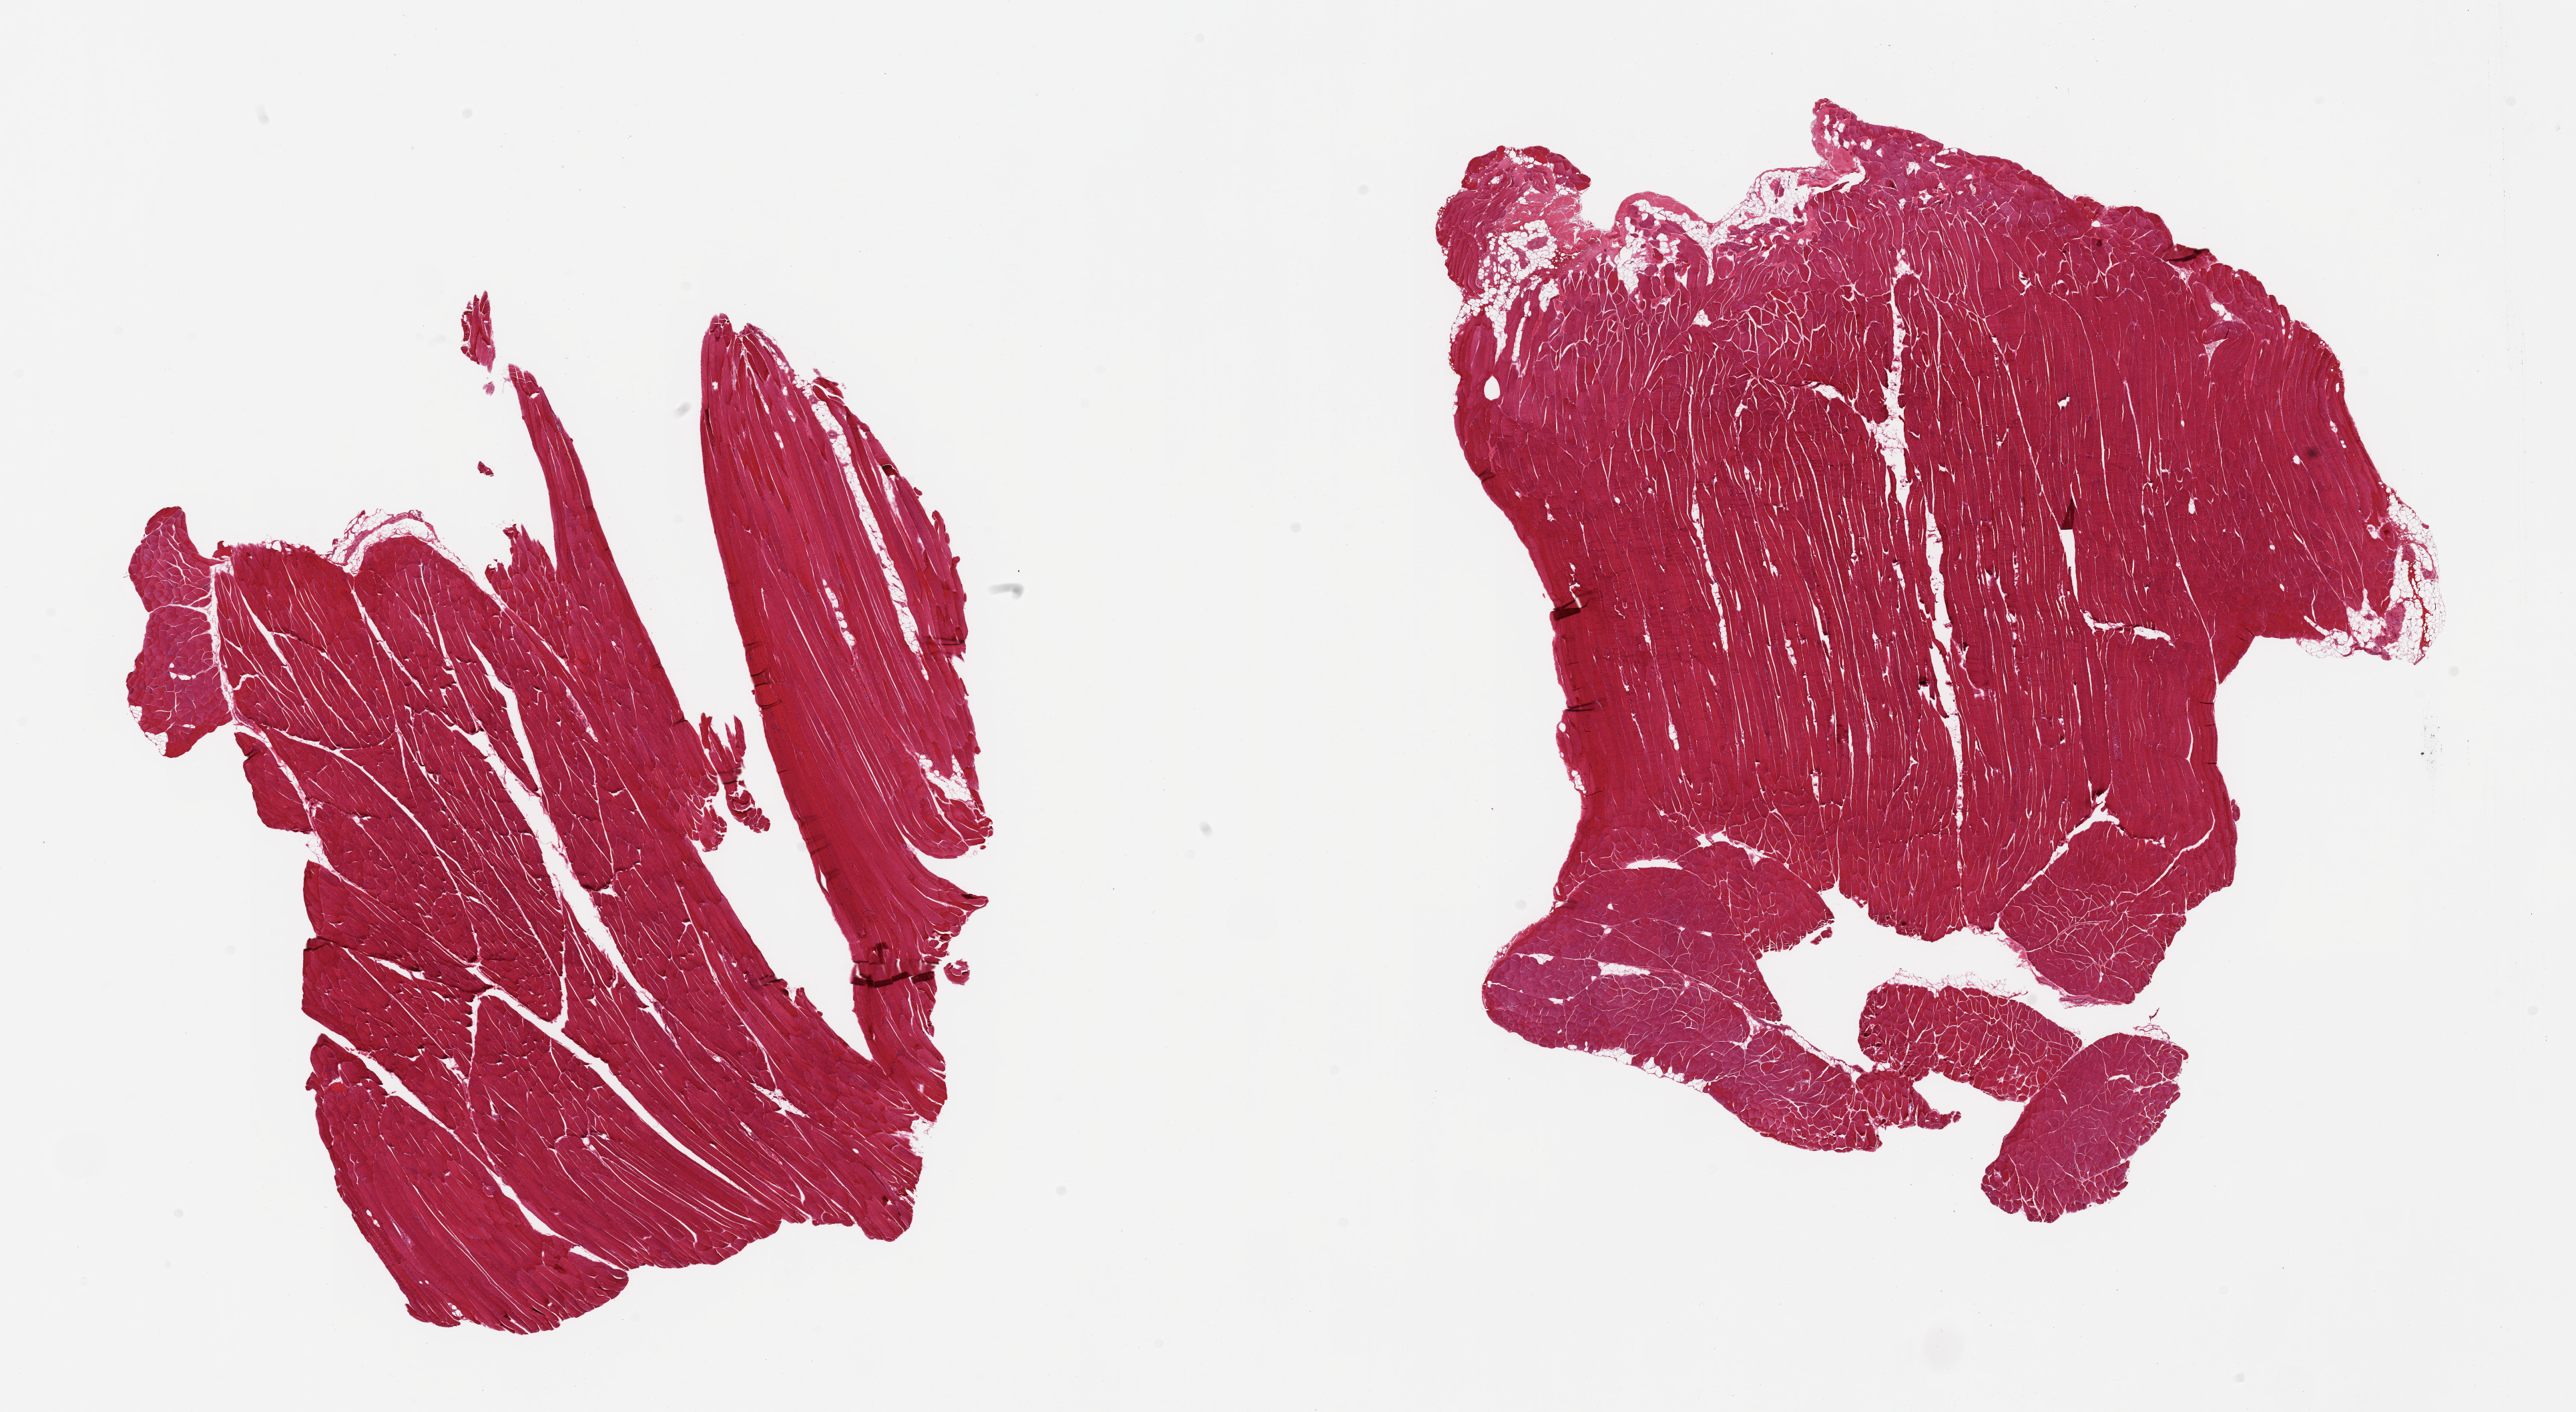
Whole-slide image, H&E stain, whole scanned area (about 30.5 x 16.7 mm) shown as a low-resolution overview, PAXgene-fixed, paraffin-embedded tissue, target tissue: skeletal muscle, tissue donor sample. Donor: male.
Reviewer comment on this tissue sample: 2 pieces; includes small portion of attached tendon and fat.